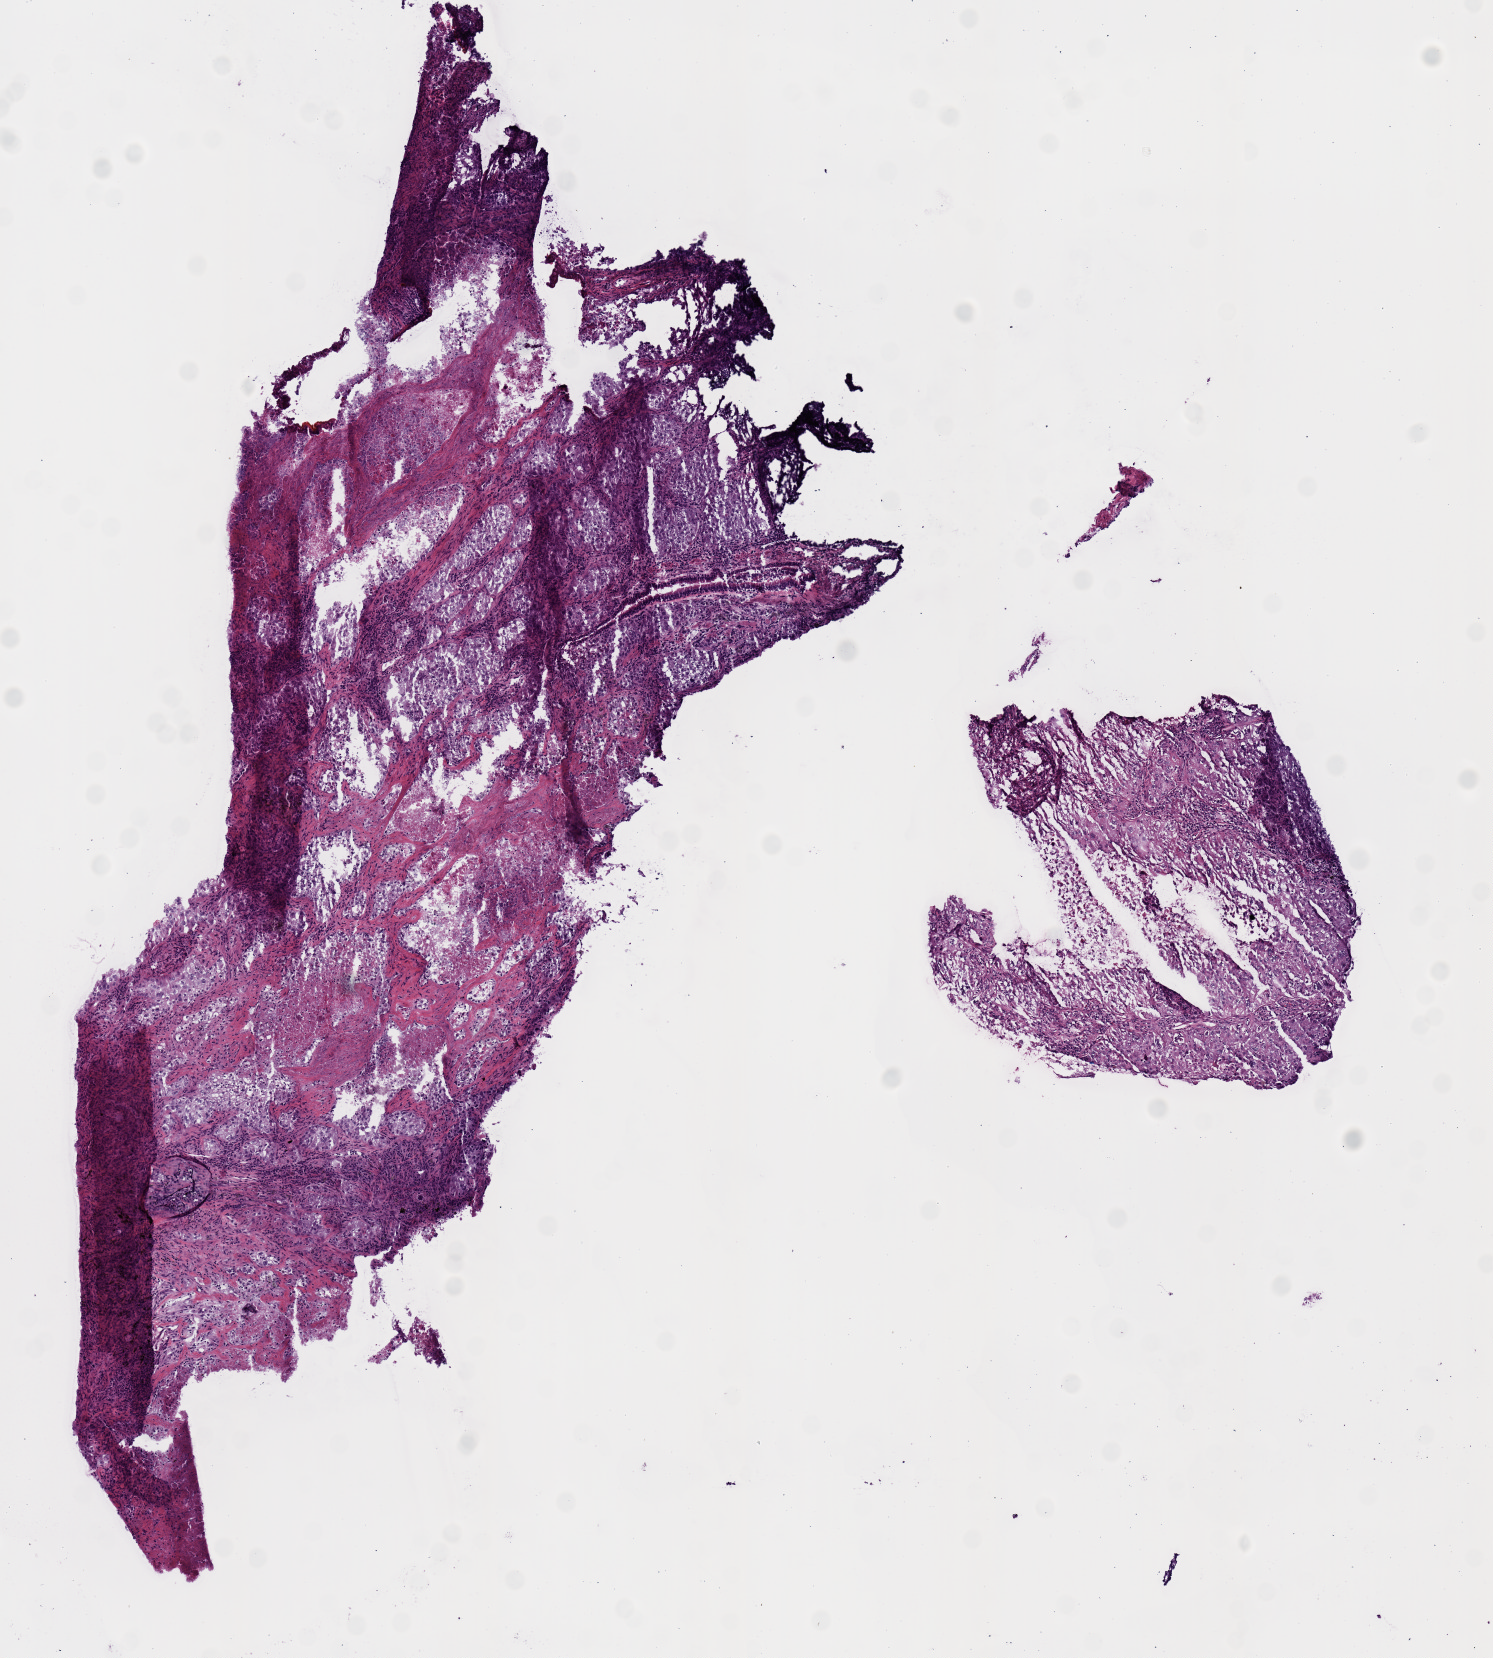
Whole-slide histology image, H&E-stained — low-resolution overview of the scanned area, about 5.9 x 6.6 mm (from a 20x scan). Frozen section. Lung, primary tumour sample. Male patient; age at initial diagnosis 59 years. Composition of this section per pathologist review: tumour cells 75%, tumour nuclei 80%, normal cells 0%, stromal cells 10%, necrosis 15%.
• AJCC pathologic stage: IIB (7th edition)
• histologic diagnosis: Adenocarcinoma with mixed subtypes